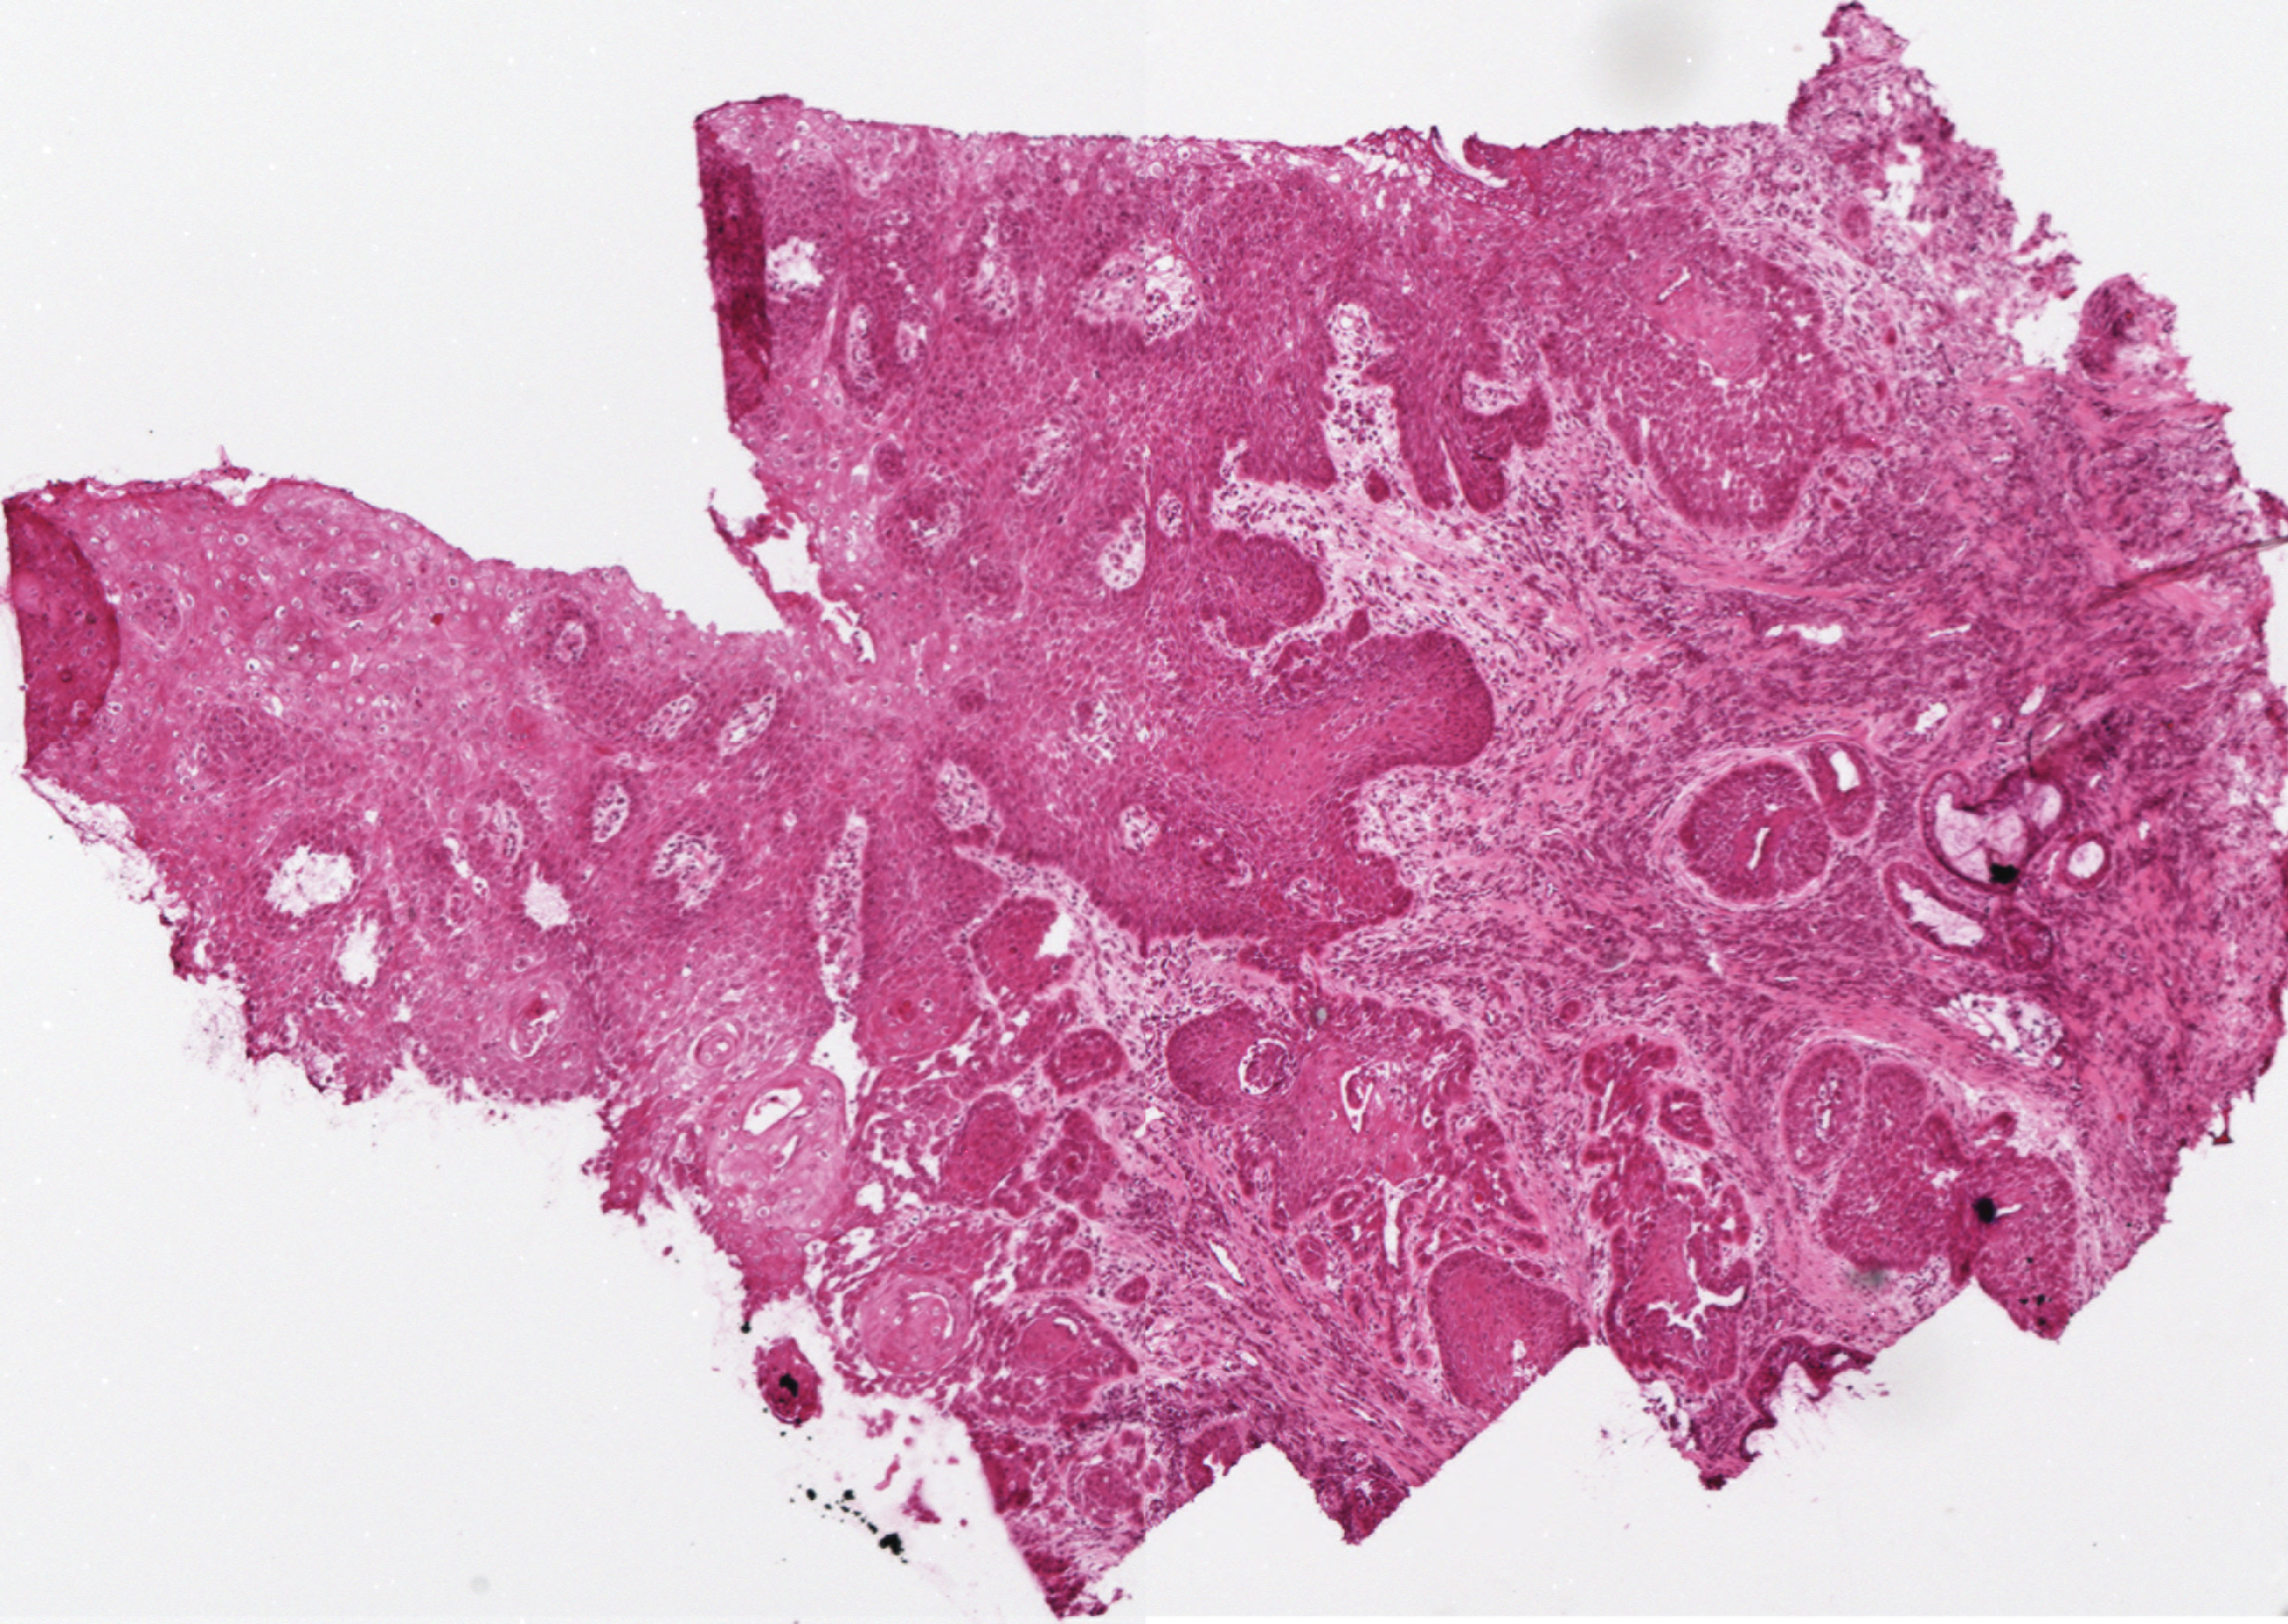
Hematoxylin and eosin (H&E) stained micrograph of a single small tissue field, covering about 1.3 x 0.9 mm, frozen section from the top of the tissue portion, sample: primary tumour, head and neck. Patient: male, age at initial diagnosis 55 years. Slide review estimates, as recorded: tumour cells 75%, tumour nuclei 75%.
Diagnosis: Squamous cell carcinoma, NOS (larynx, NOS).